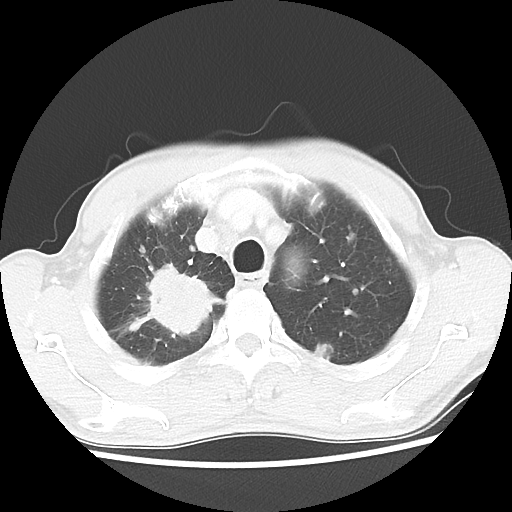
Chest CT, one axial slice; slice 43 of 52 in the series (ordered by position); reconstruction kernel LUNG; 100 kVp; lung window (W 1500 / L -600 HU); 512 × 512 image matrix, field of view 323 × 323 mm. Patient: male, 66 years. Case-level facts recorded for this patient, not image findings: clinical TNM (as recorded): T2 N0 M1a.
Outlined on this slice (bounding box drawn by a radiologist):
- lung tumour (recorded histology: adenocarcinoma): bounding box (x1, y1, x2, y2) in pixels: (126, 258, 230, 347)